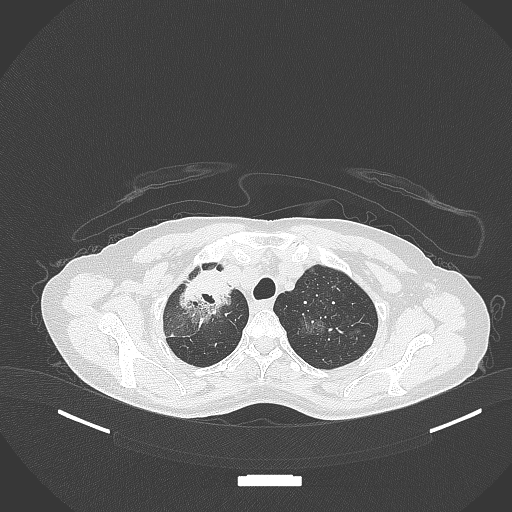
Chest CT, one axial slice. Position 274 of 284 along the scan axis. Reconstruction kernel B70f. Lung window (W 1500 / L -600 HU). 1 mm slice thickness. 512 × 512 image matrix, field of view 400 × 400 mm. Female patient, age 59 years. Case-level facts recorded for this patient, not image findings: clinical TNM (as recorded): T3 N0 M0.
Outlined on this slice (bounding box drawn by a radiologist):
- lung tumour (recorded histology: adenocarcinoma): bounding box <177,264,234,325> (left, top, right, bottom; pixels)